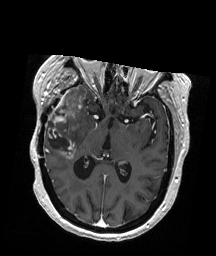
Brain MRI from a brain-tumour surgery series, one axial slice. Position 107 of 192 along the scan axis. T1-weighted post-contrast. 216 × 256 image matrix. Case-level facts recorded for this patient, not image findings: histopathology: Glioblastoma; WHO grade: 4; IDH mutation: no; tumour location: Right Temporal.
Outlined on this slice (manually delineated by an expert):
- tumour: bounding box (x1, y1, x2, y2) in pixels: (46, 86, 87, 158)